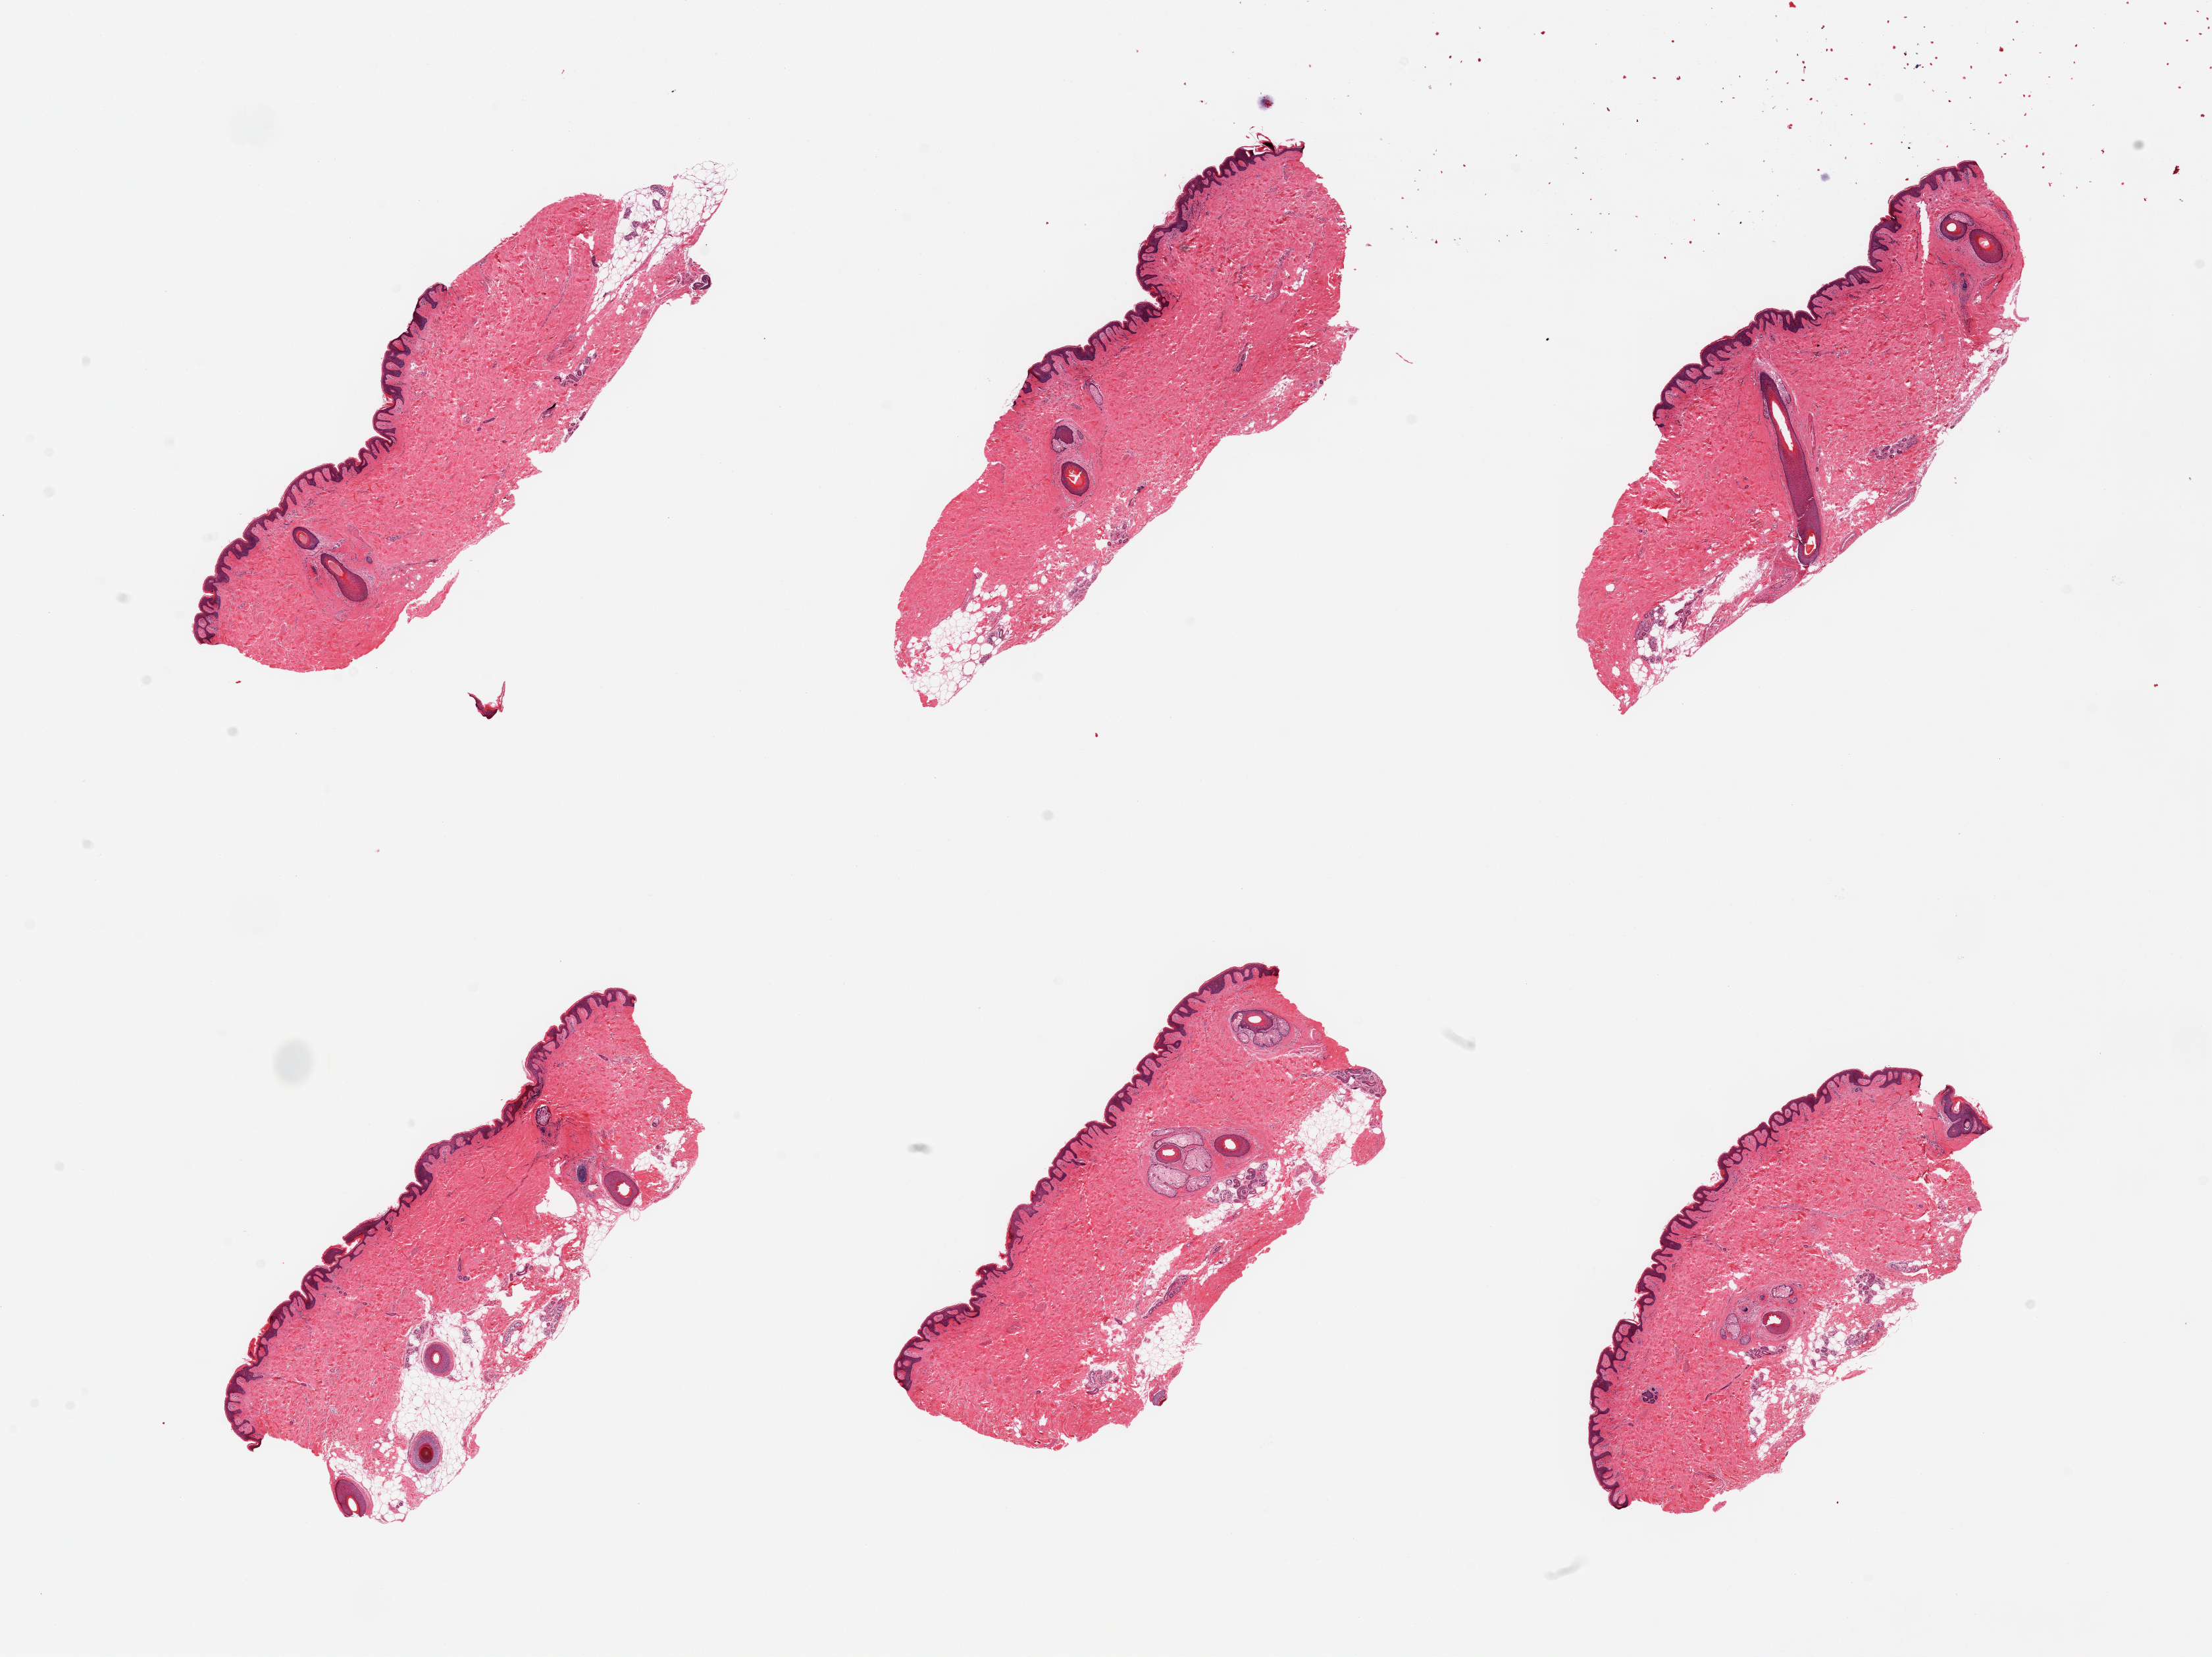
Whole-slide image, H&E stain, low-resolution overview of the scanned area, about 26.6 x 19.9 mm; PAXgene-fixed paraffin-embedded (PFPE) section; sampled site (target tissue): skin of suprapubic region; tissue donor sample. Male donor.
Review note (as recorded): 6 pieces; hair-bearing skin with up to 15% external/internal (periadnexal) fat.